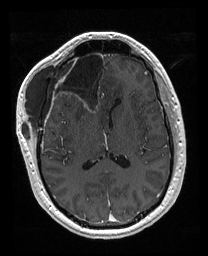
Brain MRI from a brain-tumour surgery series, one axial slice; slice 86 of 176 in the series (ordered by position); T1-weighted post-contrast; 1 mm slice thickness; 208 × 256 image matrix, field of view 208 × 256 mm. From the clinical record (not read from this slice): histopathology: Astrocytoma; WHO grade: 4; IDH mutation: yes.
Annotated regions visible in this slice (manually delineated by an expert):
- previous resection cavity: bounding box <56,52,106,111> (left, top, right, bottom; pixels)